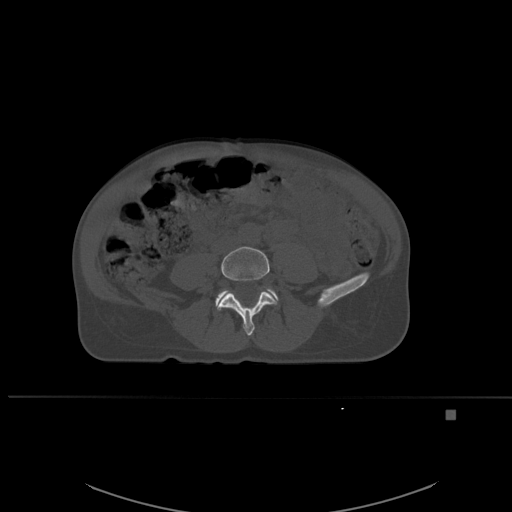
CT including the spine, one axial slice; position 187 of 537 along the scan axis; bone window (W 1800 / L 400 HU); 512 × 512 image matrix, field of view 440 × 440 mm. Female patient, age 45 years. Case-level facts recorded for this patient, not image findings: primary cancer: lung.
Outlined on this slice (semi-automatically segmented with operator editing):
- L4 vertebra: bounding box (x1, y1, x2, y2) in pixels: (216, 246, 278, 336)
- L5 vertebra: (215, 288, 278, 304)